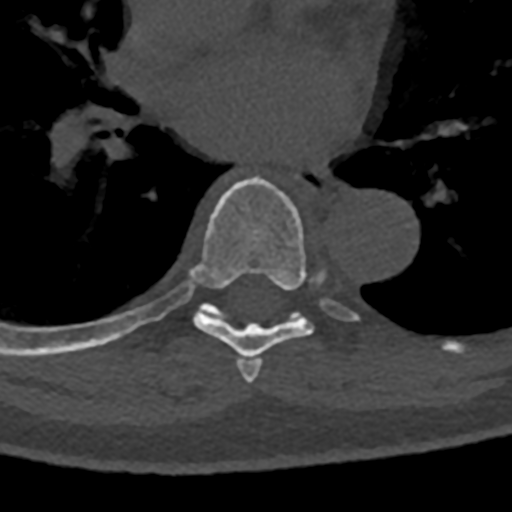
CT including the spine, one axial slice. Position 755 of 797 along the scan axis. Reconstruction kernel Br40s/3. 120 kVp. Bone window (W 1800 / L 400 HU). 0.5 mm slice thickness. 512 × 512 image matrix, field of view 160 × 160 mm. Patient: male, 74 years. From the clinical record (not read from this slice): primary cancer: renal; vertebrae with lytic lesions (as recorded): T10, L1, L2, L3, L4, L5.
Outlined on this slice (semi-automatically segmented with operator editing):
- T6 vertebra: bounding box <242,358,263,383> (left, top, right, bottom; pixels)
- T7 vertebra: <71,176,358,369>
- T8 vertebra: <70,306,209,352>